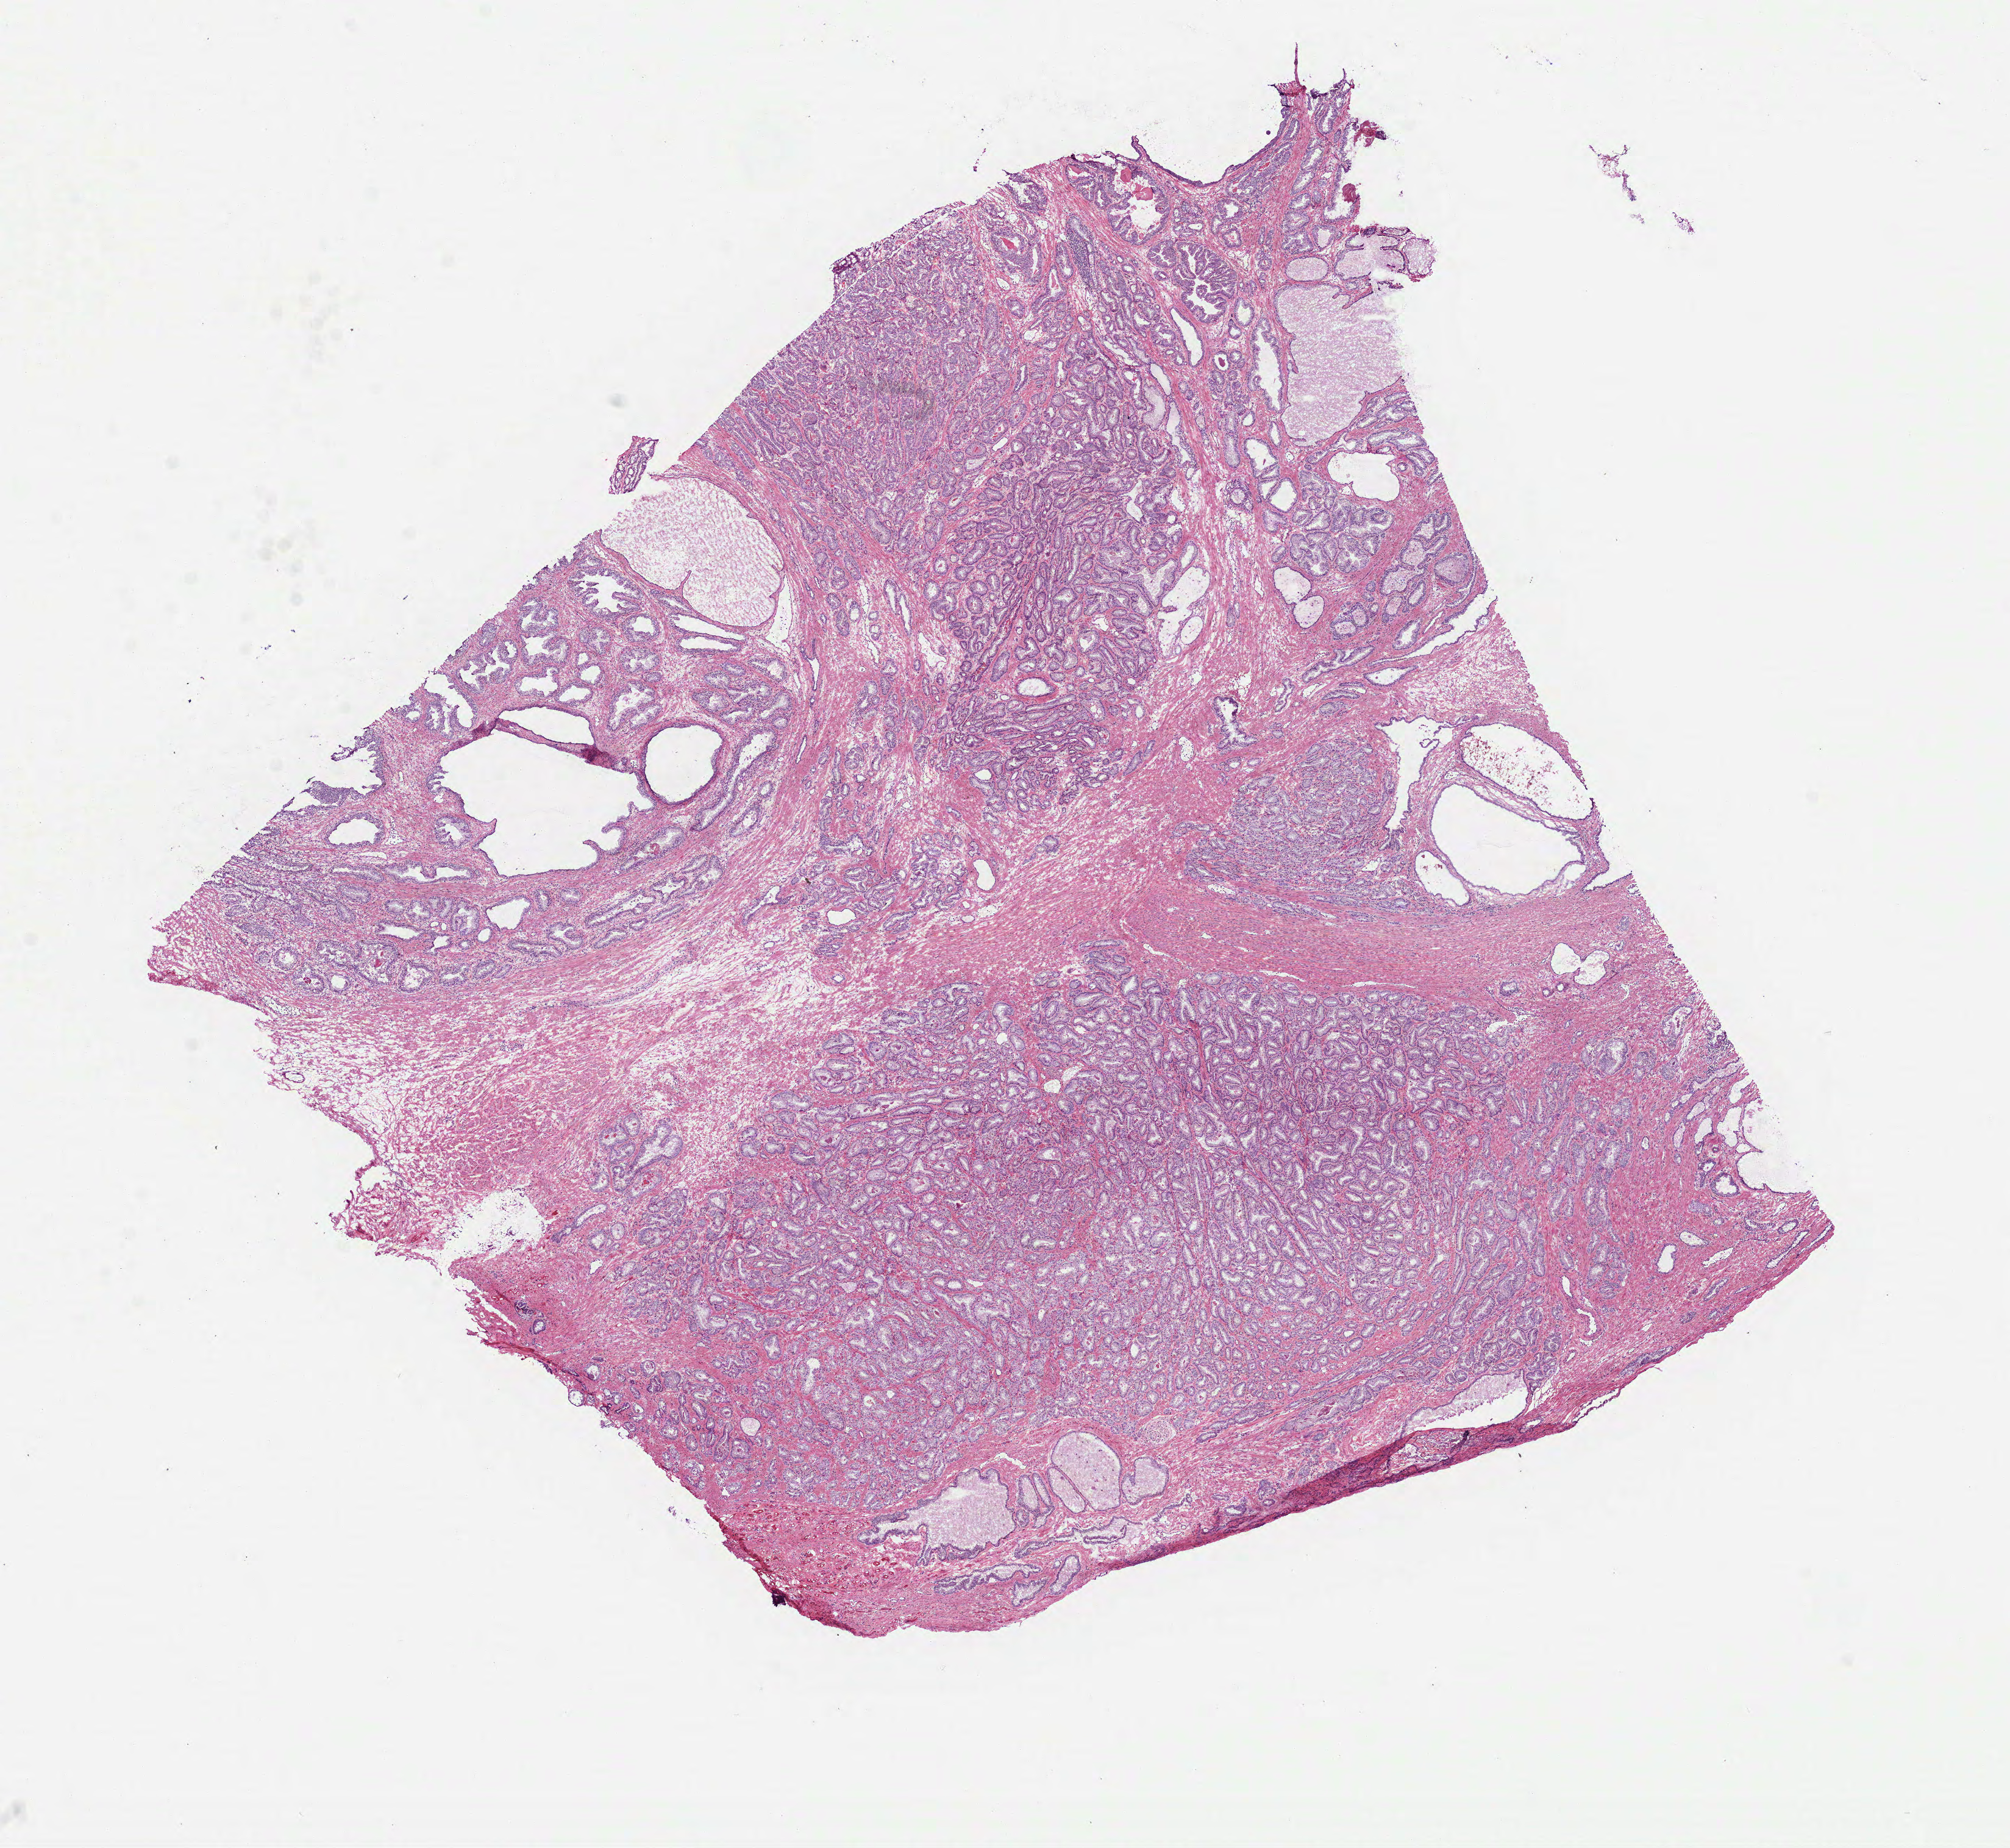
Whole-slide histology image, Hematoxylin and eosin (H&E) stained — a low-resolution overview of the entire scanned area, about 13.3 x 12.2 mm. Frozen section. Prostate, primary tumour sample. Patient: male, age at initial diagnosis 62 years. Gleason score: 7 (3+4). Pathologist review of this section (percent, as recorded): tumour cells 70%, tumour nuclei 80%, normal cells 5%, stromal cells 25%, necrosis 0%. Inflammatory infiltration, as recorded: lymphocyte infiltration 0%, monocyte infiltration 0%, neutrophil infiltration 0%.
- lymph nodes positive (case pathology): 0 of 5 examined
- histologic diagnosis: Acinar cell carcinoma (prostate gland)